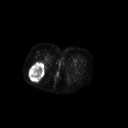
FDG PET of an extremity soft-tissue mass (from a PET/CT study), one axial slice. Position 46 of 267 along the scan axis. 3.27 mm slice thickness. 128 × 128 image matrix, field of view 700 × 700 mm. Patient: female, 70 years. Case-level facts recorded for this patient, not image findings: histological type: synovial sarcoma; grade: intermediate; site of the primary tumour: right buttock.
Annotated regions visible in this slice (expert contour drawn on MRI and transferred to this co-registered scan by the dataset authors):
- gross tumour volume including surrounding oedema: bounding box (x1, y1, x2, y2) in pixels: (29, 62, 45, 81)
- gross tumour volume (mass): (29, 62, 45, 81)